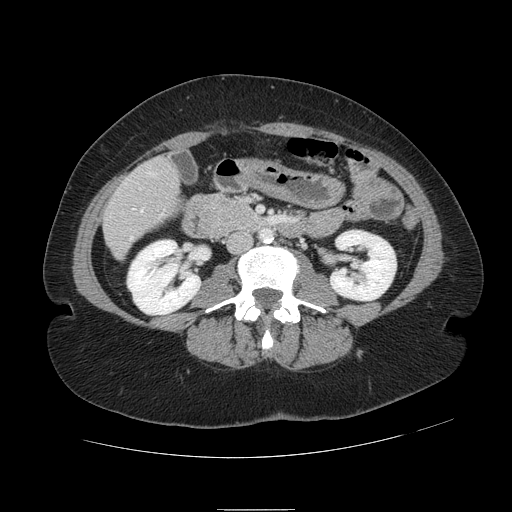
Contrast-enhanced abdominal CT, one axial slice. Slice 21 of 121 in the series (ordered by position). 120 kVp. Intravenous contrast given. Soft-tissue window (W 400 / L 40 HU). 2.5 mm slice thickness. 512 × 512 image matrix. Female patient, age 52 years. From the clinical record (not read from this slice): diagnosis: colorectal cancer liver metastases, imaged before liver resection; multiple liver metastases: yes; largest metastasis: 6.3 cm; disease in both lobes: no.
Outlined on this slice (expert manual segmentation):
- hepatic veins: bounding box <130,172,153,239> (left, top, right, bottom; pixels)
- liver: <105,160,177,257>
- portal vein (with intrahepatic branches): <133,208,135,210>